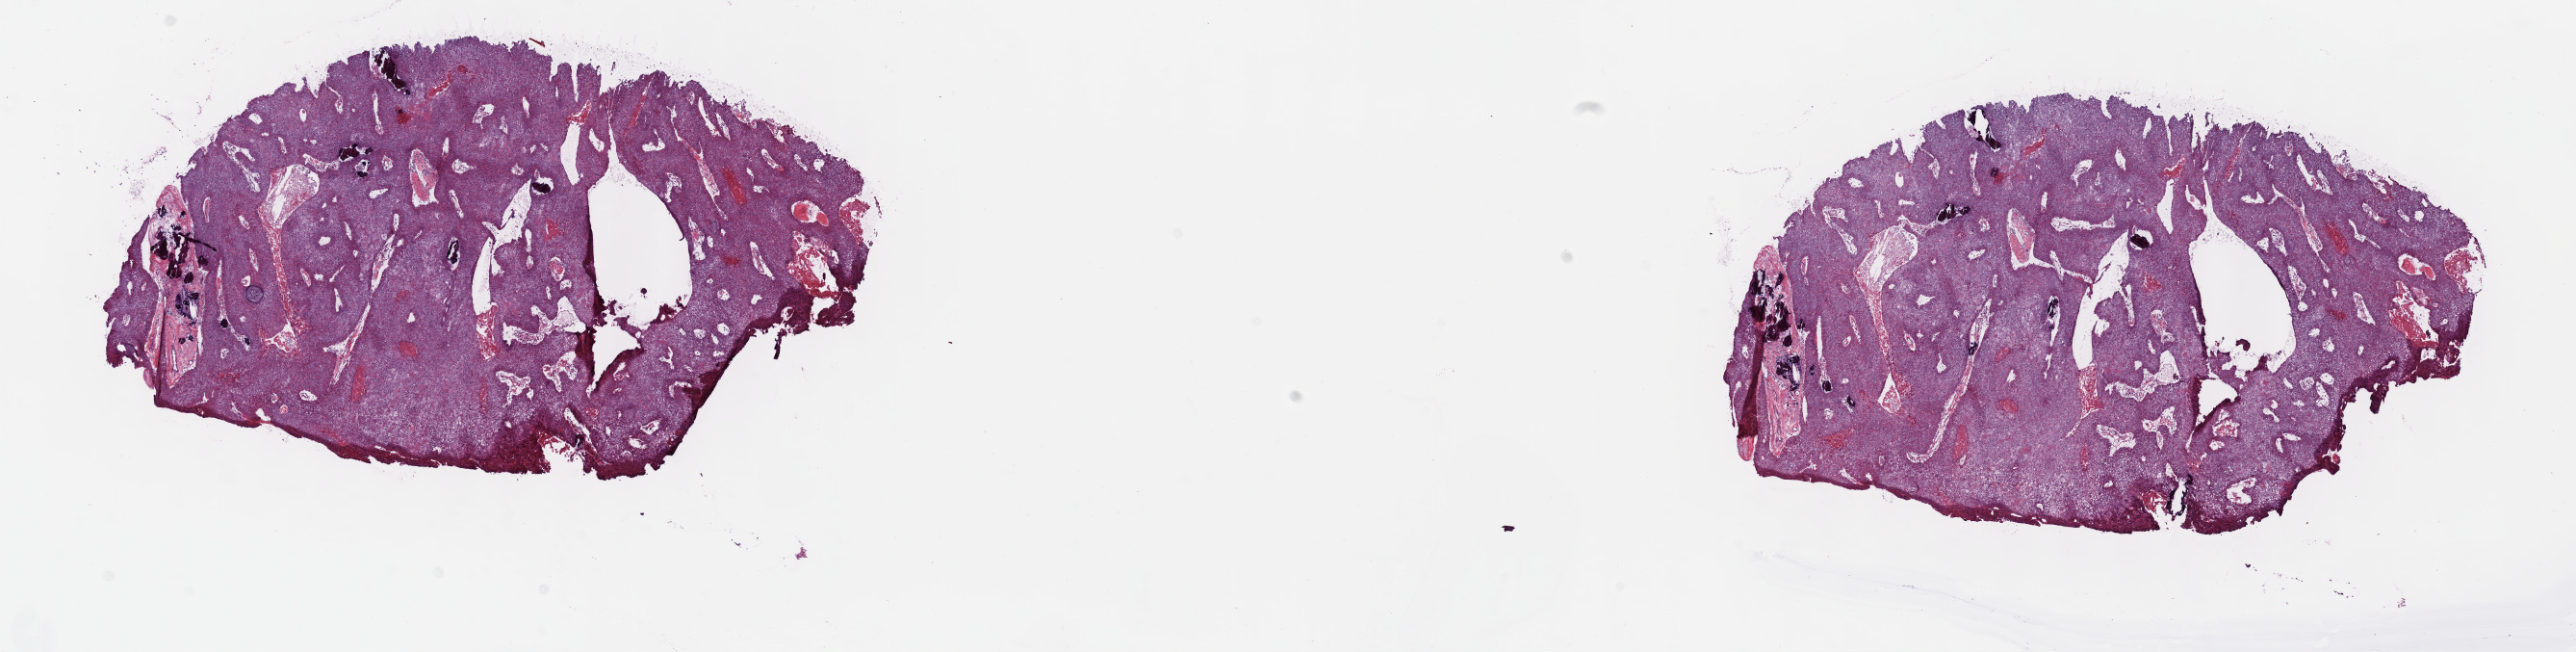
Whole-slide histology image, Hematoxylin and eosin (H&E) stained — whole scanned area (about 21.6 x 5.5 mm, from a 40x scan) shown as a low-resolution overview; frozen section from the top of the tissue portion; thymus, primary tumour sample. Patient: female, age at initial diagnosis 40 years. Slide review estimates, as recorded: tumour cells 90%, tumour nuclei 95%, normal cells 0%, stromal cells 10%, necrosis 0%. Infiltration values recorded for this section: lymphocyte infiltration 0%, monocyte infiltration 0%, neutrophil infiltration 0%.
Histologic diagnosis: Thymoma, type B3, malignant.